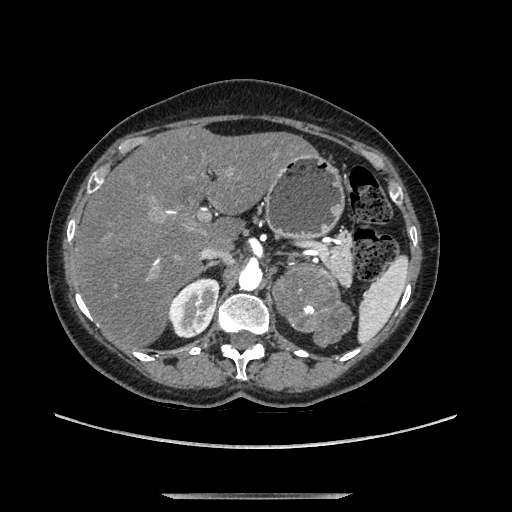
Contrast-enhanced abdominal CT, one axial slice; position 83 of 169 along the scan axis; soft-tissue window (W 400 / L 40 HU); 1.25 mm slice thickness; 512 × 512 image matrix, field of view 400 × 400 mm. Female patient. From the clinical record (not read from this slice): diagnosis: adrenocortical carcinoma; tumour side: left adrenal; tumour size at pathology: 9 cm; Ki-67 index: 2 %; stage (as recorded): 3.
Outlined on this slice (semi-automatically segmented with operator editing):
- mass: bounding box <277,269,349,344> (left, top, right, bottom; pixels)